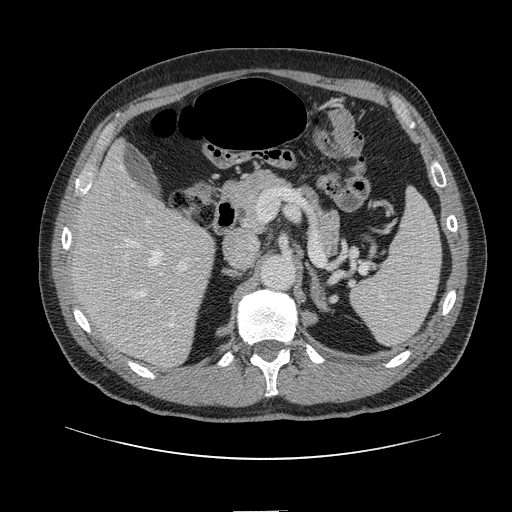
Contrast-enhanced abdominal CT, one axial slice. Position 74 of 161 along the scan axis. Intravenous contrast given. Soft-tissue window (W 400 / L 40 HU). 2.5 mm slice thickness. 512 × 512 image matrix, field of view 412 × 412 mm. Male patient, age 66 years. From the clinical record (not read from this slice): diagnosis: colorectal cancer liver metastases, imaged before liver resection; multiple liver metastases: no; largest metastasis: 3.5 cm.
Structures marked on this image (expert manual segmentation):
- hepatic veins: bounding box (x1, y1, x2, y2) in pixels: (119, 165, 173, 327)
- liver: (75, 146, 214, 366)
- planned liver remnant (the part of the liver to remain after resection): (75, 146, 195, 292)
- portal vein (with intrahepatic branches): (123, 219, 191, 306)